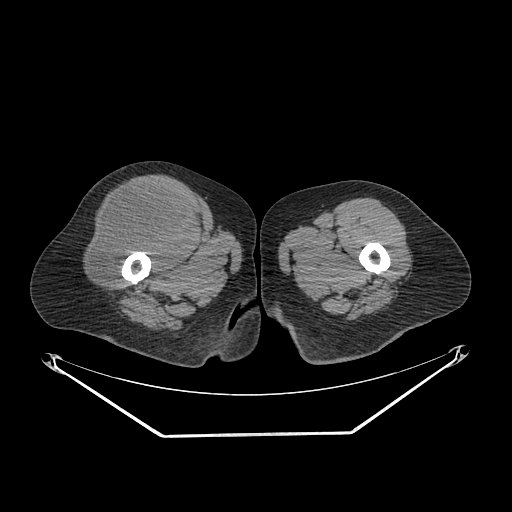
CT of an extremity soft-tissue mass (from a PET/CT study), one axial slice. Position 262 of 311 along the scan axis. Reconstruction kernel SOFT. 140 kVp. Soft-tissue window (W 400 / L 40 HU). 3.75 mm slice thickness. 512 × 512 image matrix, field of view 500 × 500 mm. Female patient. From the clinical record (not read from this slice): histological type: pleiomorphic undifferentiated sarcoma; grade: high; site of the primary tumour: right quadricep.
Outlined on this slice (expert contour drawn on MRI and transferred to this co-registered scan by the dataset authors):
- tumour plus oedema (research contour): bounding box <91,185,193,282> (left, top, right, bottom; pixels)
- tumour (research contour): <91,185,193,282>